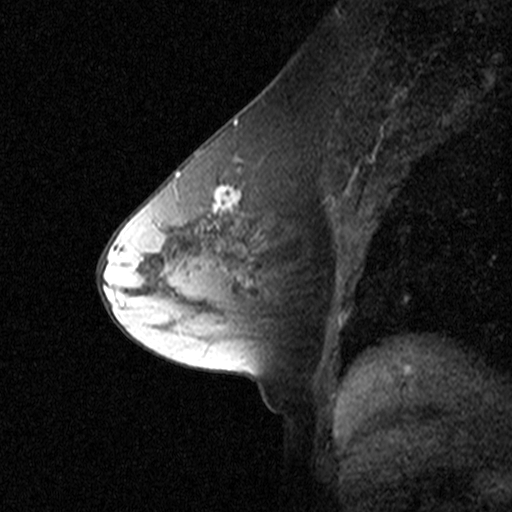
Breast MRI (dynamic contrast-enhanced), one sagittal slice; position 24 of 44 along the scan axis; dynamic contrast-enhanced study with each time point stored as its own series, time point 2 of 3 at this slice position (early post-contrast, ordered by acquisition time); 1.5 T; TE 4.5 ms, TR 11 ms; 3 mm slice thickness; 512 × 512 image matrix. Female patient, age 53 years. From the clinical record (not read from this slice): setting: breast cancer imaged before/during neoadjuvant chemotherapy; receptor status: HR-positive, HER2-negative.
Structures marked on this image (semi-automatically segmented with operator editing):
- analysis volume of interest (the breast-tissue region the enhancement analysis was run in; not a lesion): bounding box <170,150,277,273> (left, top, right, bottom; pixels)
- tumour enhancement mask (voxels above the 90 % enhancement threshold inside the analysis volume of interest): <176,171,241,223>